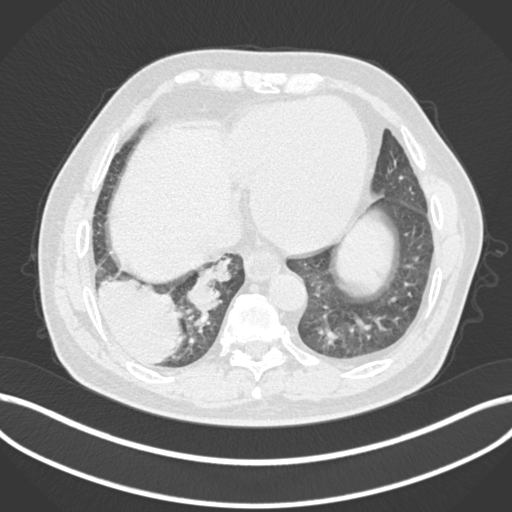
Chest CT, one axial slice; slice 35 of 200 in the series (ordered by position); reconstruction kernel B30f; 120 kVp; lung window (W 1500 / L -600 HU); 1 mm slice thickness; 512 × 512 image matrix, field of view 400 × 400 mm. Male patient, age 59 years.
Outlined on this slice (rectangle marked by the reading radiologist):
- lung tumour (recorded histology: adenocarcinoma): bounding box (x1, y1, x2, y2) in pixels: (97, 276, 187, 369)